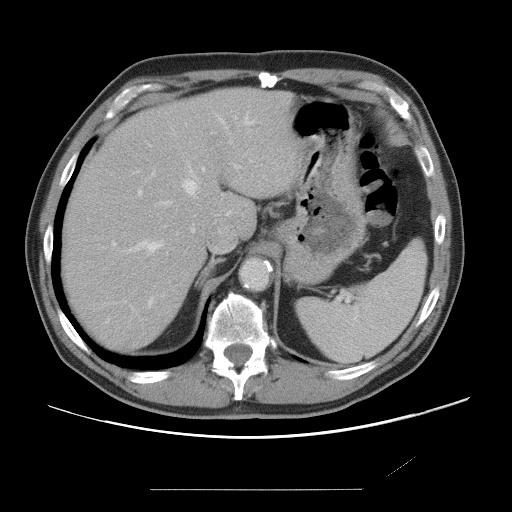
Contrast-enhanced abdominal CT, one axial slice; slice 54 of 87 in the series (ordered by position); intravenous contrast given; soft-tissue window (W 400 / L 40 HU); 512 × 512 image matrix. Male patient, age 74 years. Case-level facts recorded for this patient, not image findings: diagnosis: colorectal cancer liver metastases, imaged before liver resection; multiple liver metastases: yes.
Outlined on this slice (expert manual segmentation):
- hepatic veins: bounding box (x1, y1, x2, y2) in pixels: (130, 116, 254, 305)
- liver: (63, 90, 298, 351)
- planned liver remnant (the part of the liver to remain after resection): (63, 89, 298, 351)
- portal vein (with intrahepatic branches): (112, 164, 241, 245)